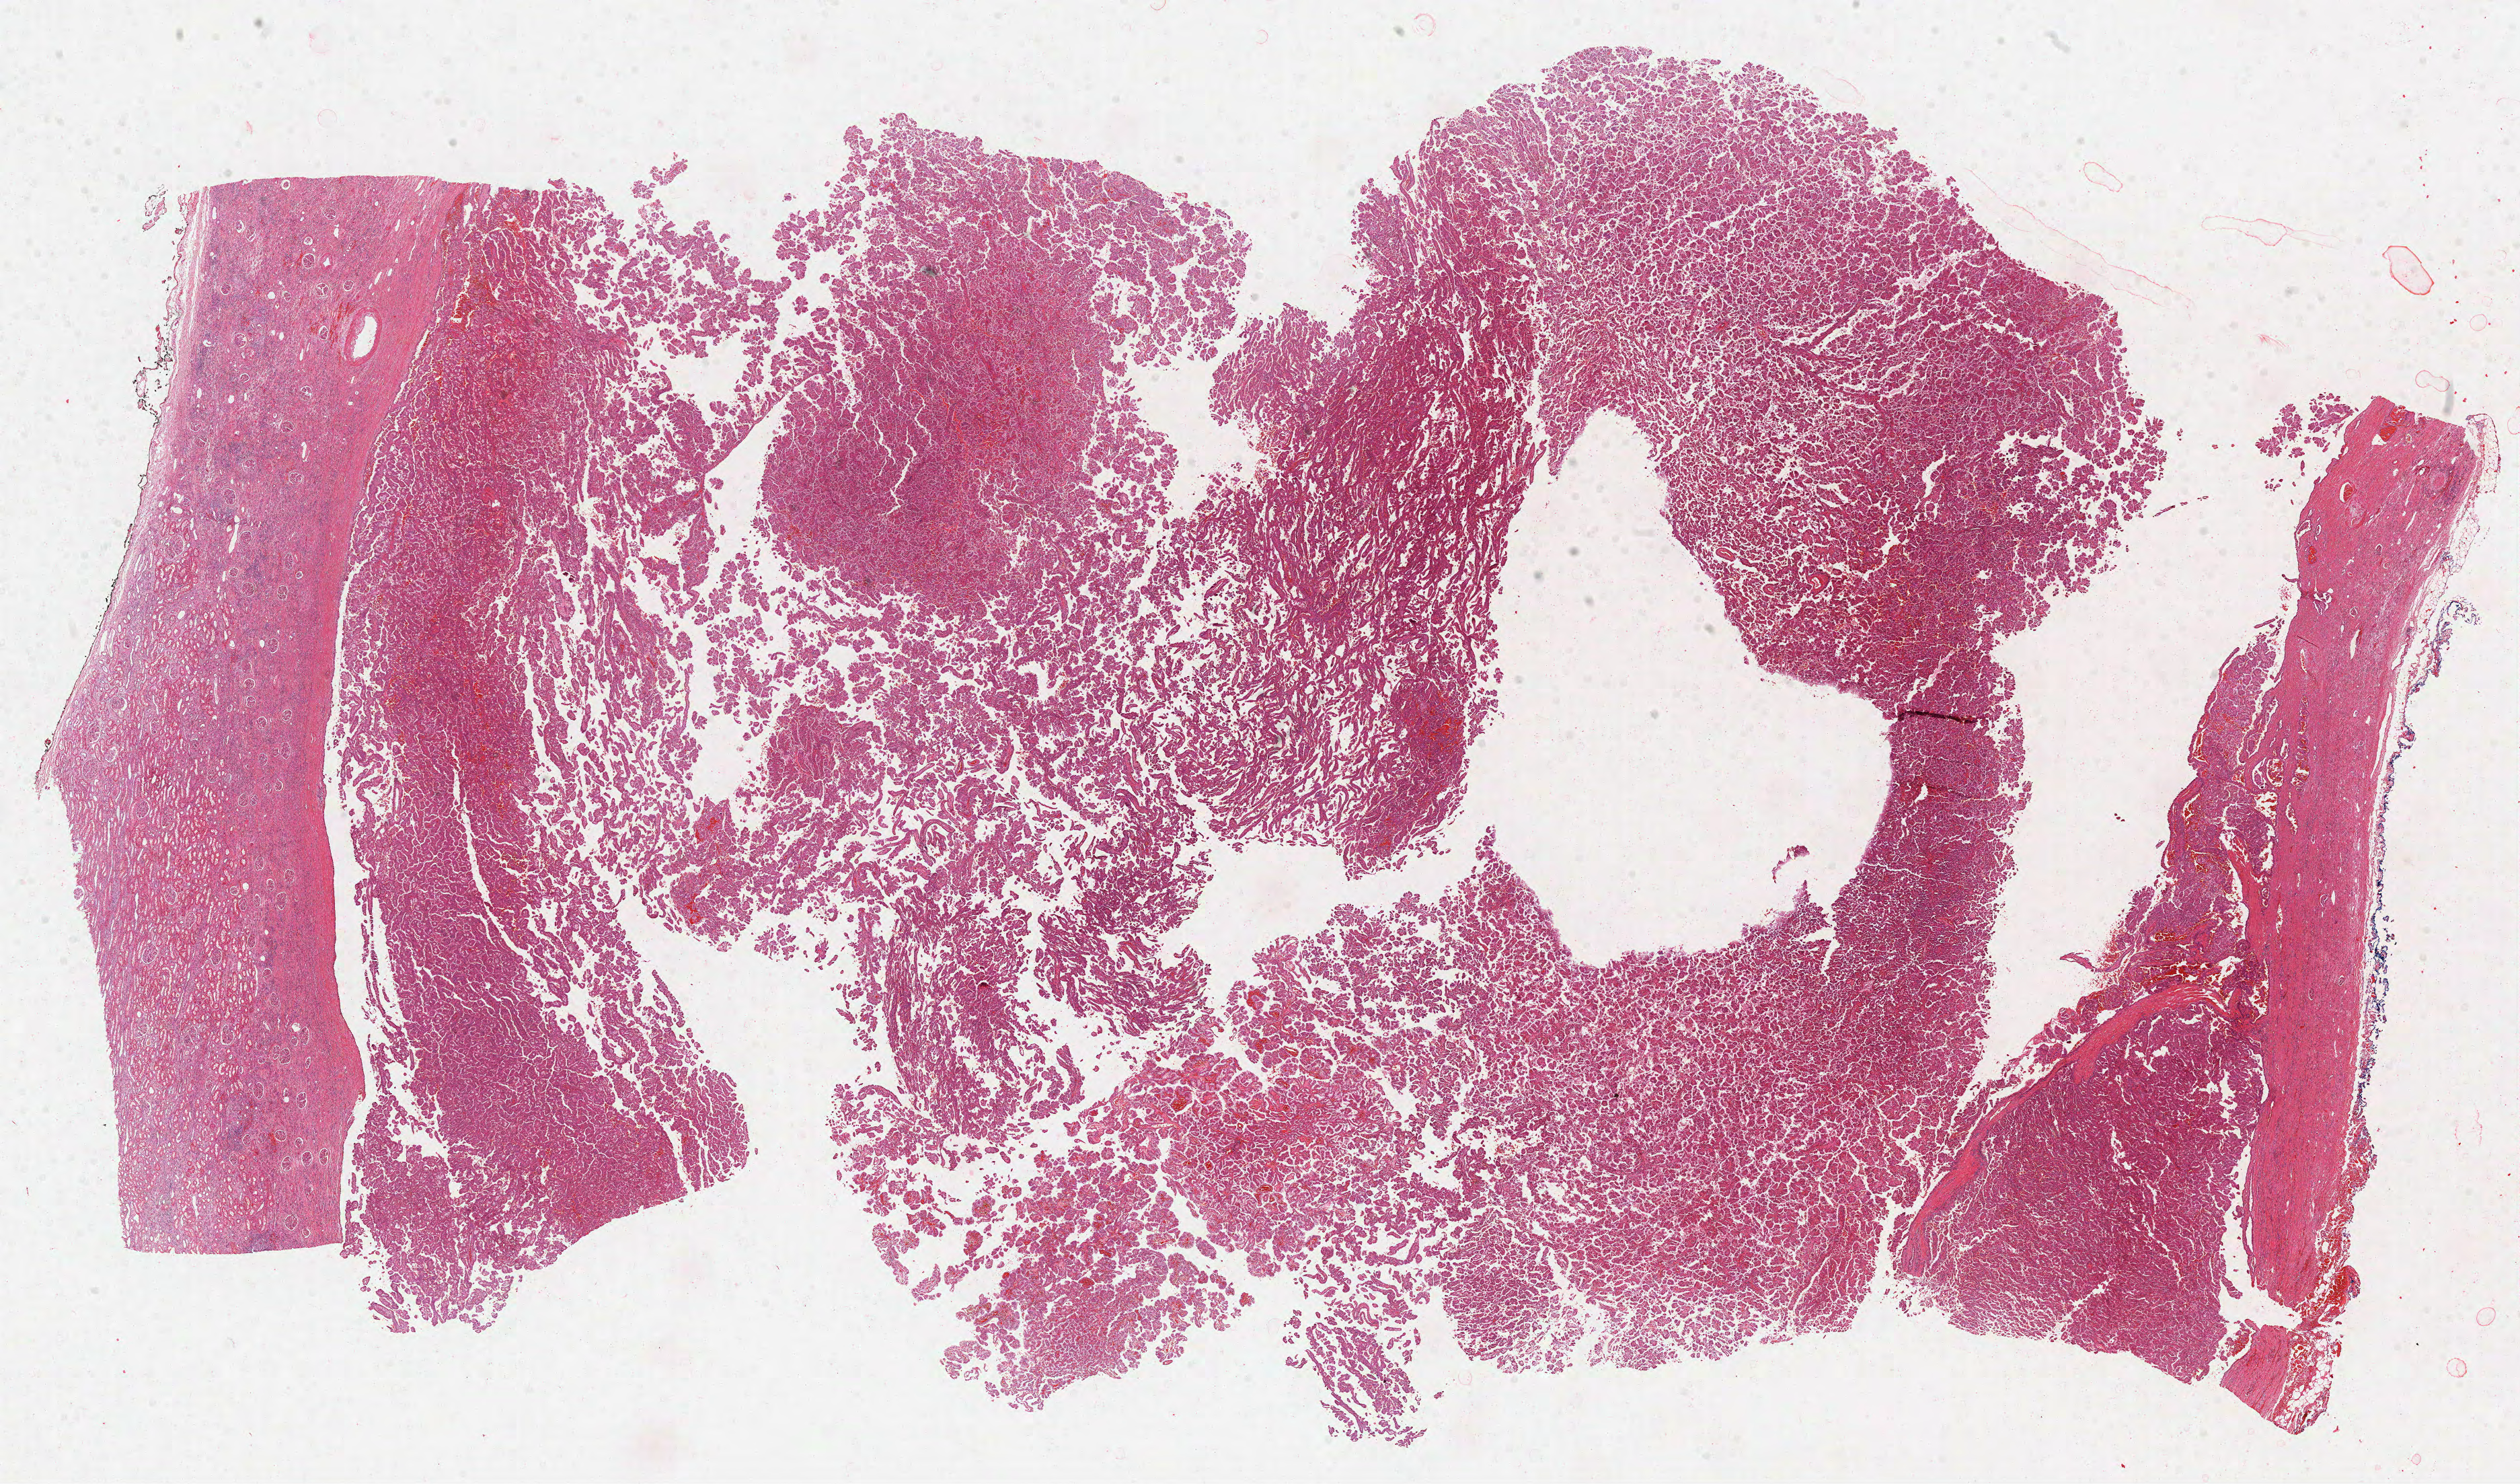
H&E whole-slide image, low-resolution overview of the scanned area, about 30.2 x 17.8 mm (slide scanned at 40x); formalin-fixed paraffin-embedded (FFPE) diagnostic section; kidney, primary tumour sample. Patient: male, age at initial diagnosis 40 years.
Diagnosis: Papillary adenocarcinoma, NOS.